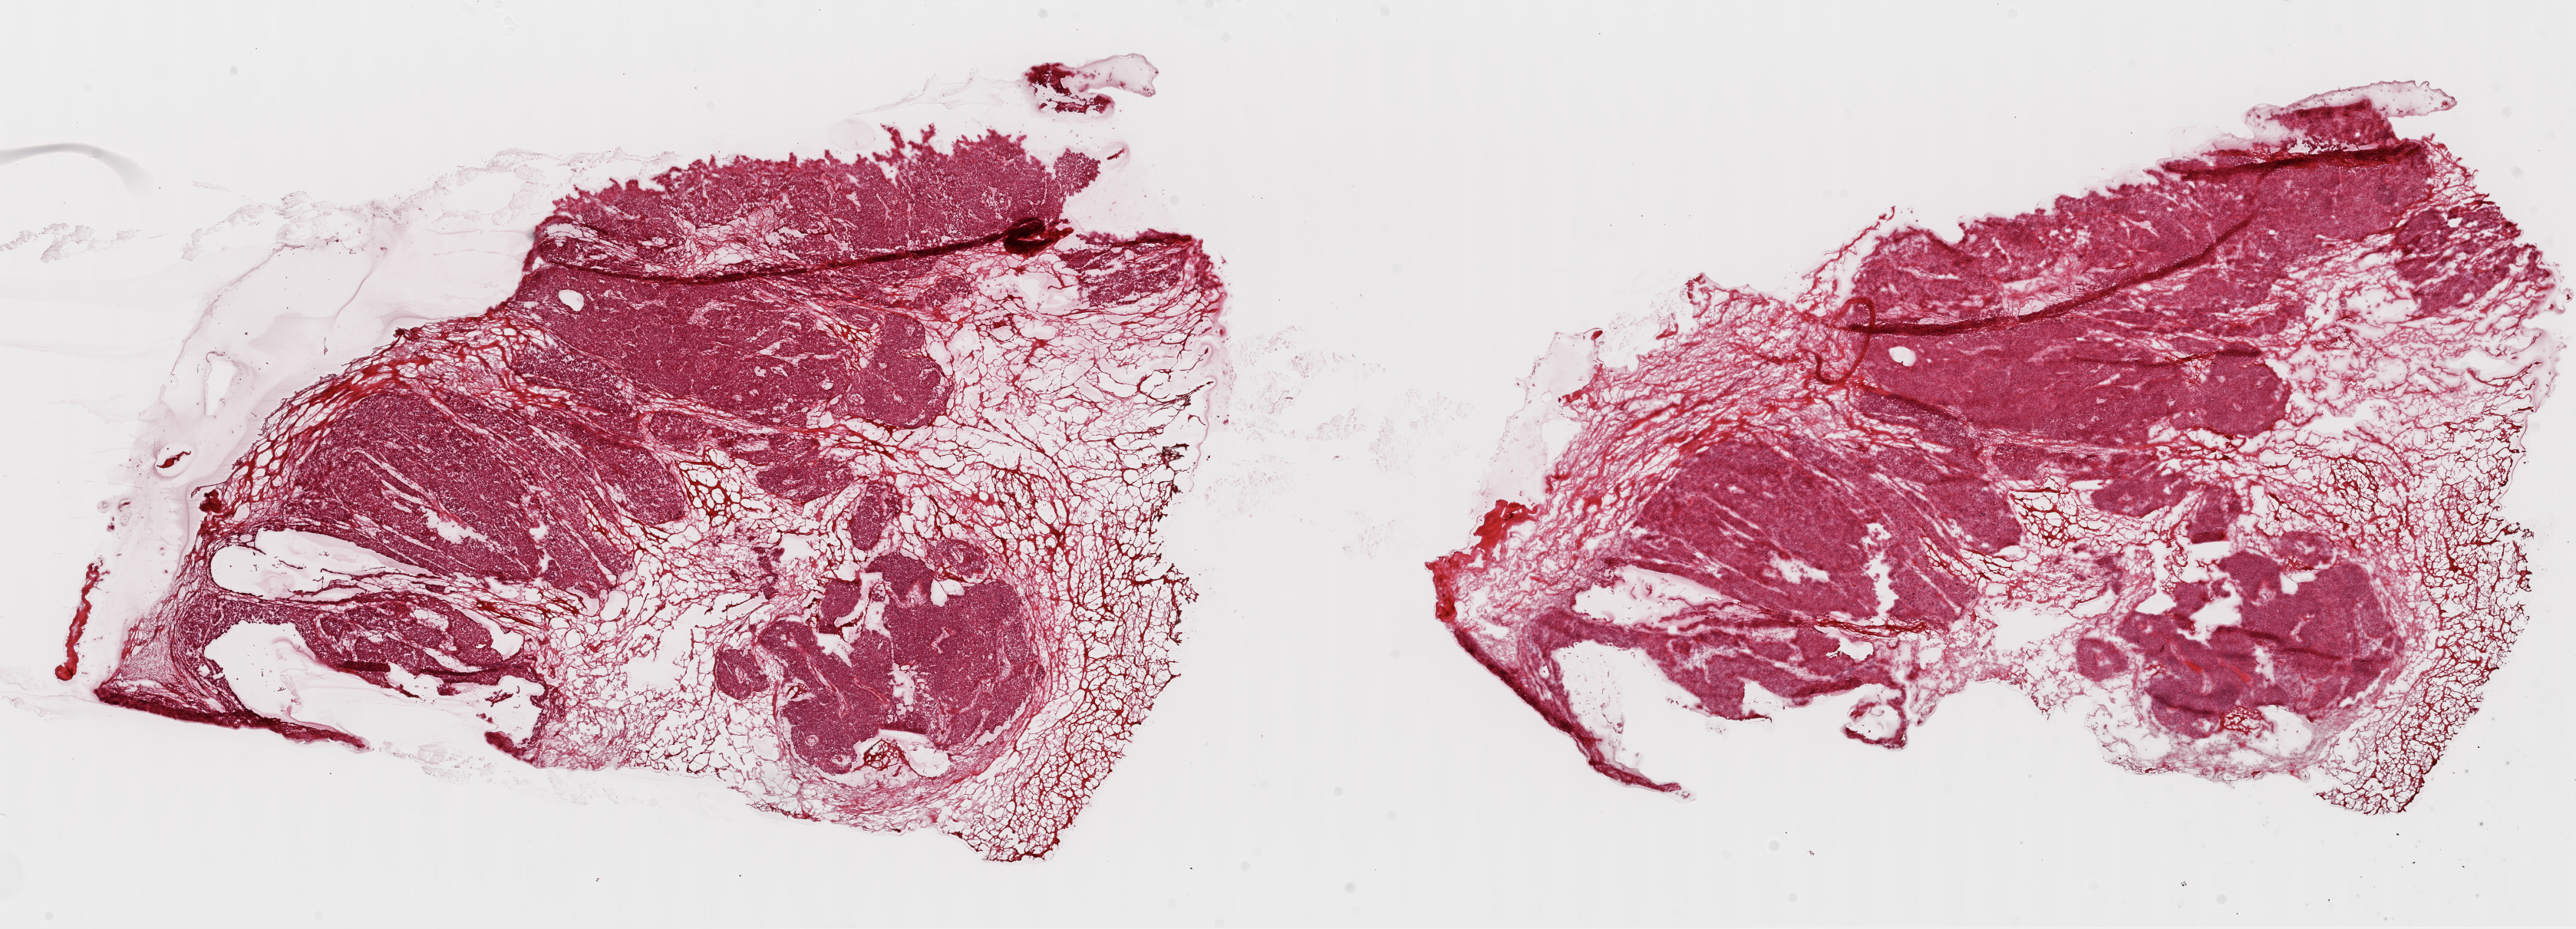
H&E-stained whole-slide image — low-resolution overview of the scanned area, about 27.1 x 9.8 mm (acquisition: 20x scan). Frozen section. Primary tumour sample from the ovary. Patient: female, age at initial diagnosis 56 years. Histologic grade: G3 (poorly differentiated). Slide review estimates, as recorded: tumour nuclei 80%, necrosis 1%.
• laterality: left
• FIGO stage: IV
• histologic diagnosis: Serous cystadenocarcinoma, NOS